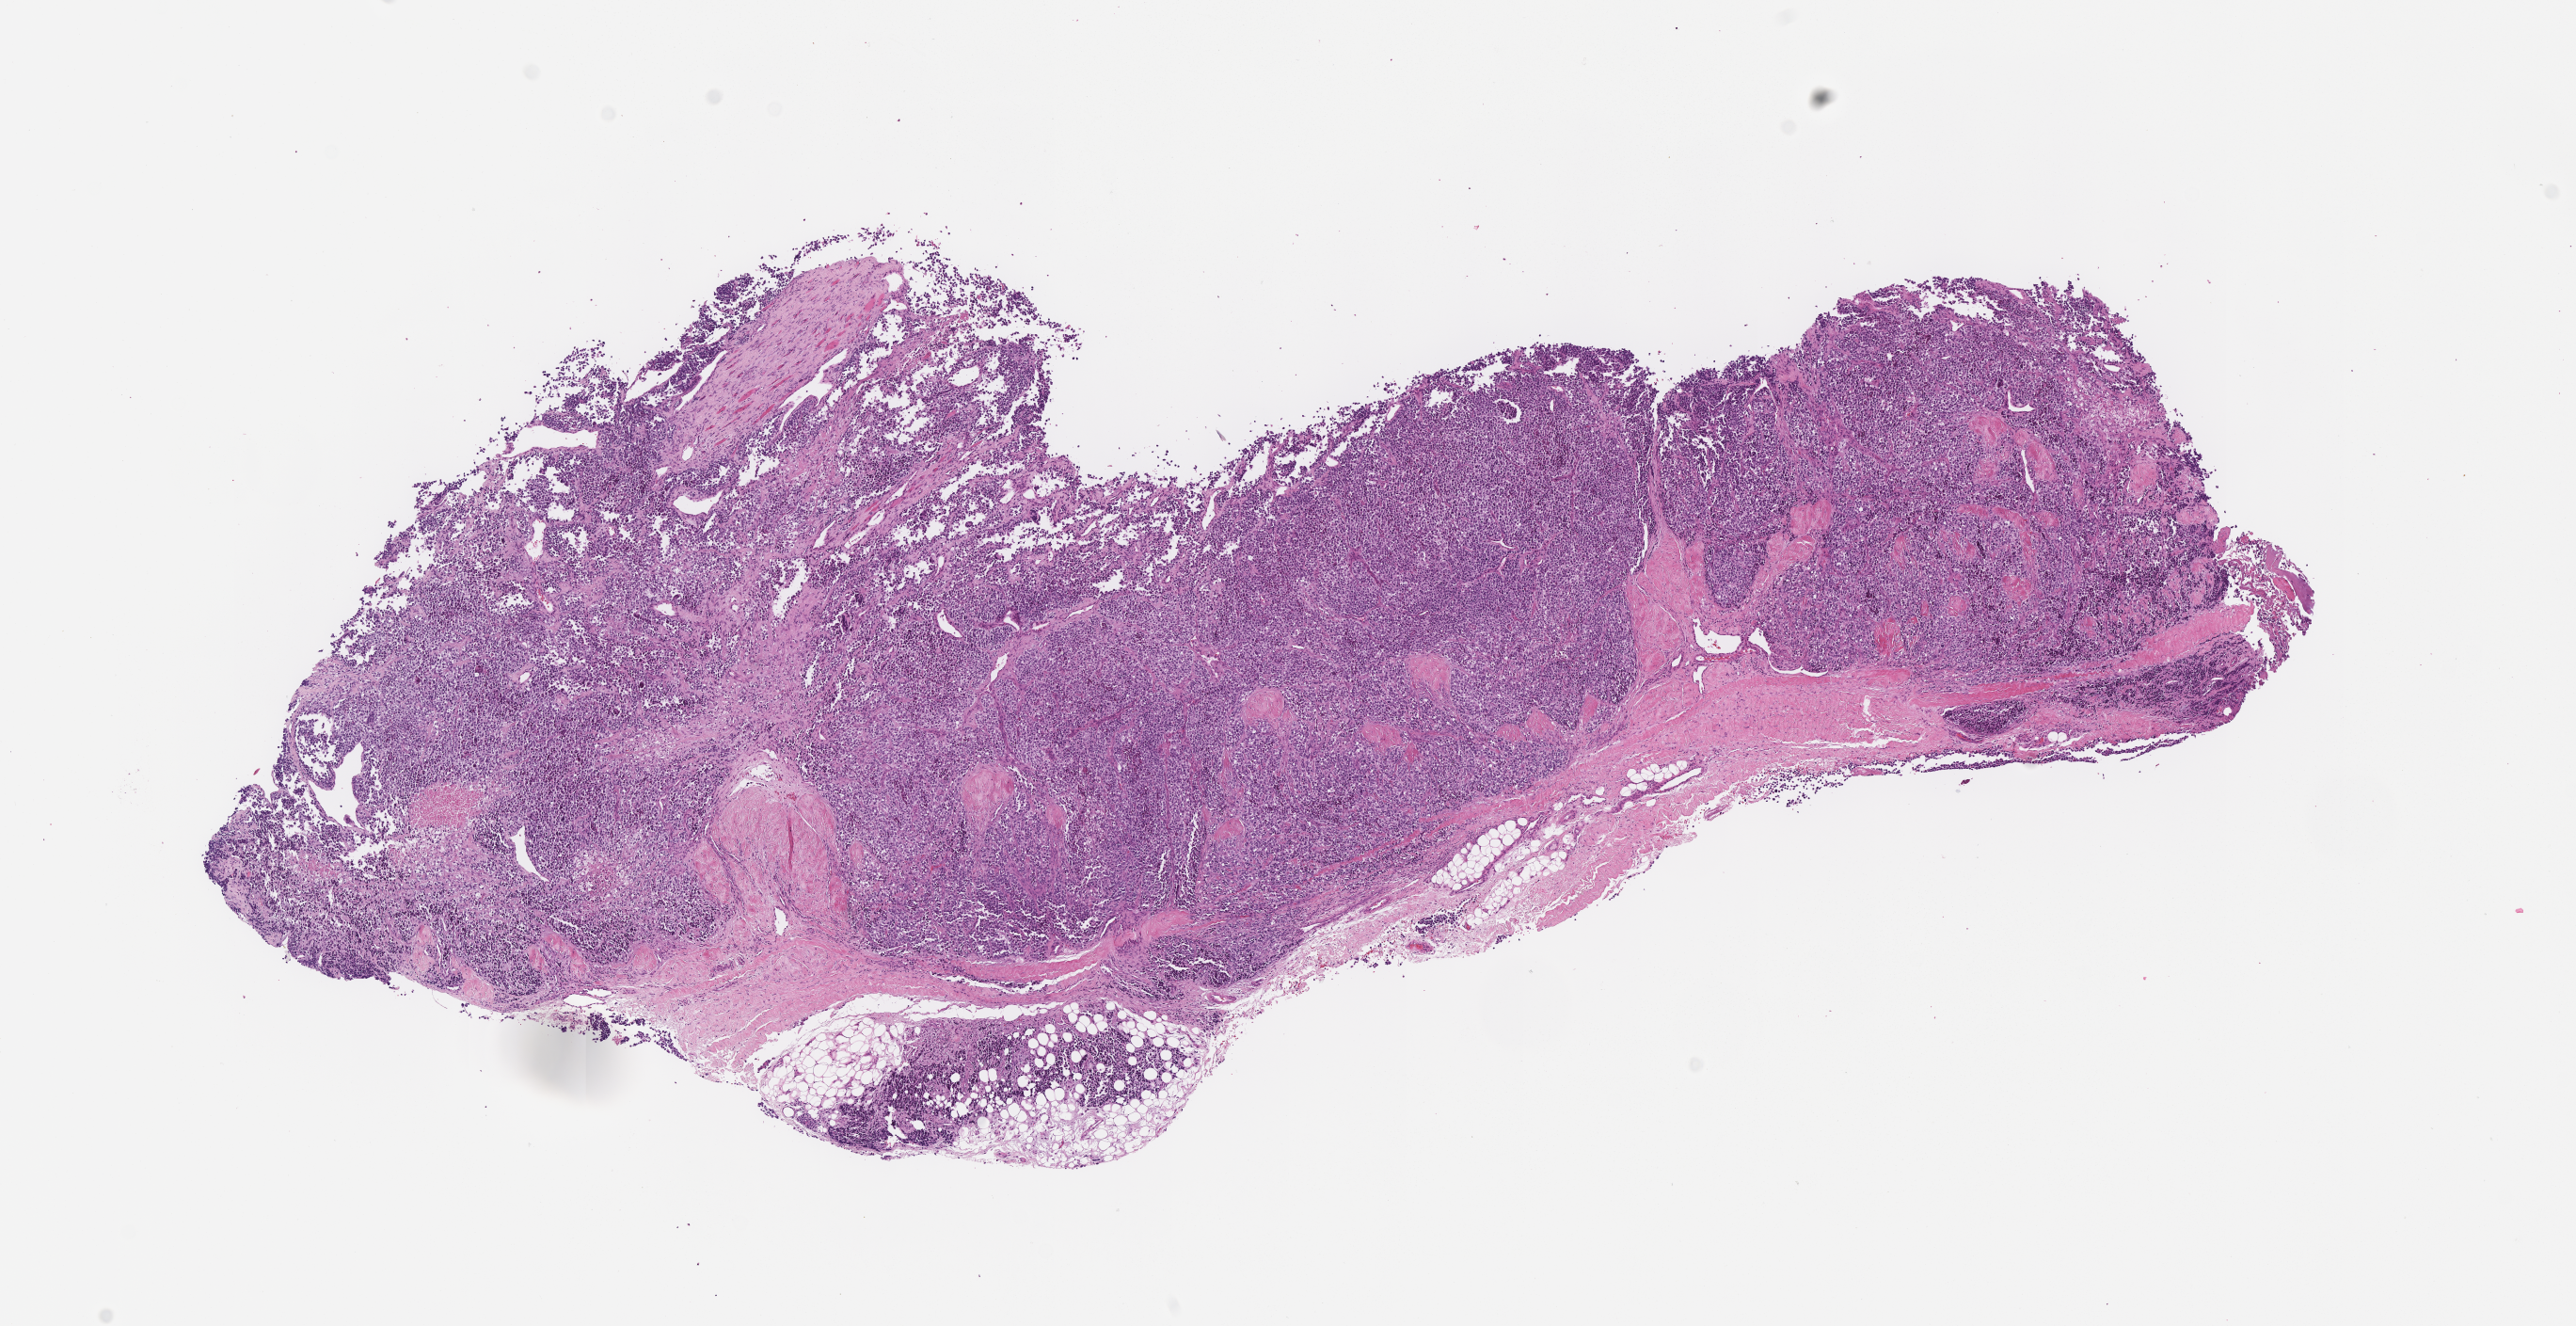
Whole-slide image, haematoxylin and eosin stain of tumor tissue — low-resolution overview of the scanned area, about 11.1 x 5.7 mm, formalin-fixed, paraffin-embedded (FFPE) tissue, site: foot, right. Female patient, age at diagnosis 10.1 years.
* diagnosis: rhabdomyosarcoma; histological classification: alveolar rhabdomyosarcoma
* stage (as recorded): 2
* metastatic status at presentation (as recorded): non-metastatic